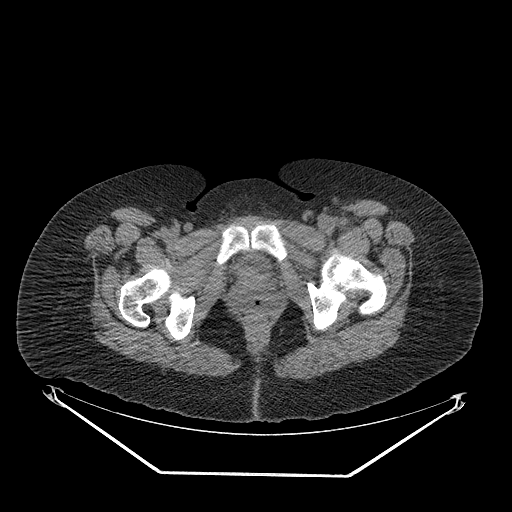
CT of an extremity soft-tissue mass (from a PET/CT study), one axial slice. Slice 54 of 267 in the series (ordered by position). Reconstruction kernel STANDARD. 140 kVp. Soft-tissue window (W 400 / L 40 HU). 3.75 mm slice thickness. 512 × 512 image matrix, field of view 500 × 500 mm. Female patient. Case-level facts recorded for this patient, not image findings: histological type: myxofibrosarcoma; grade: intermediate; site of the primary tumour: left thigh.
Structures marked on this image (expert contour drawn on MRI and transferred to this co-registered scan by the dataset authors):
- gross tumour volume including surrounding oedema: box from (x=270, y=221) to (x=355, y=250) px